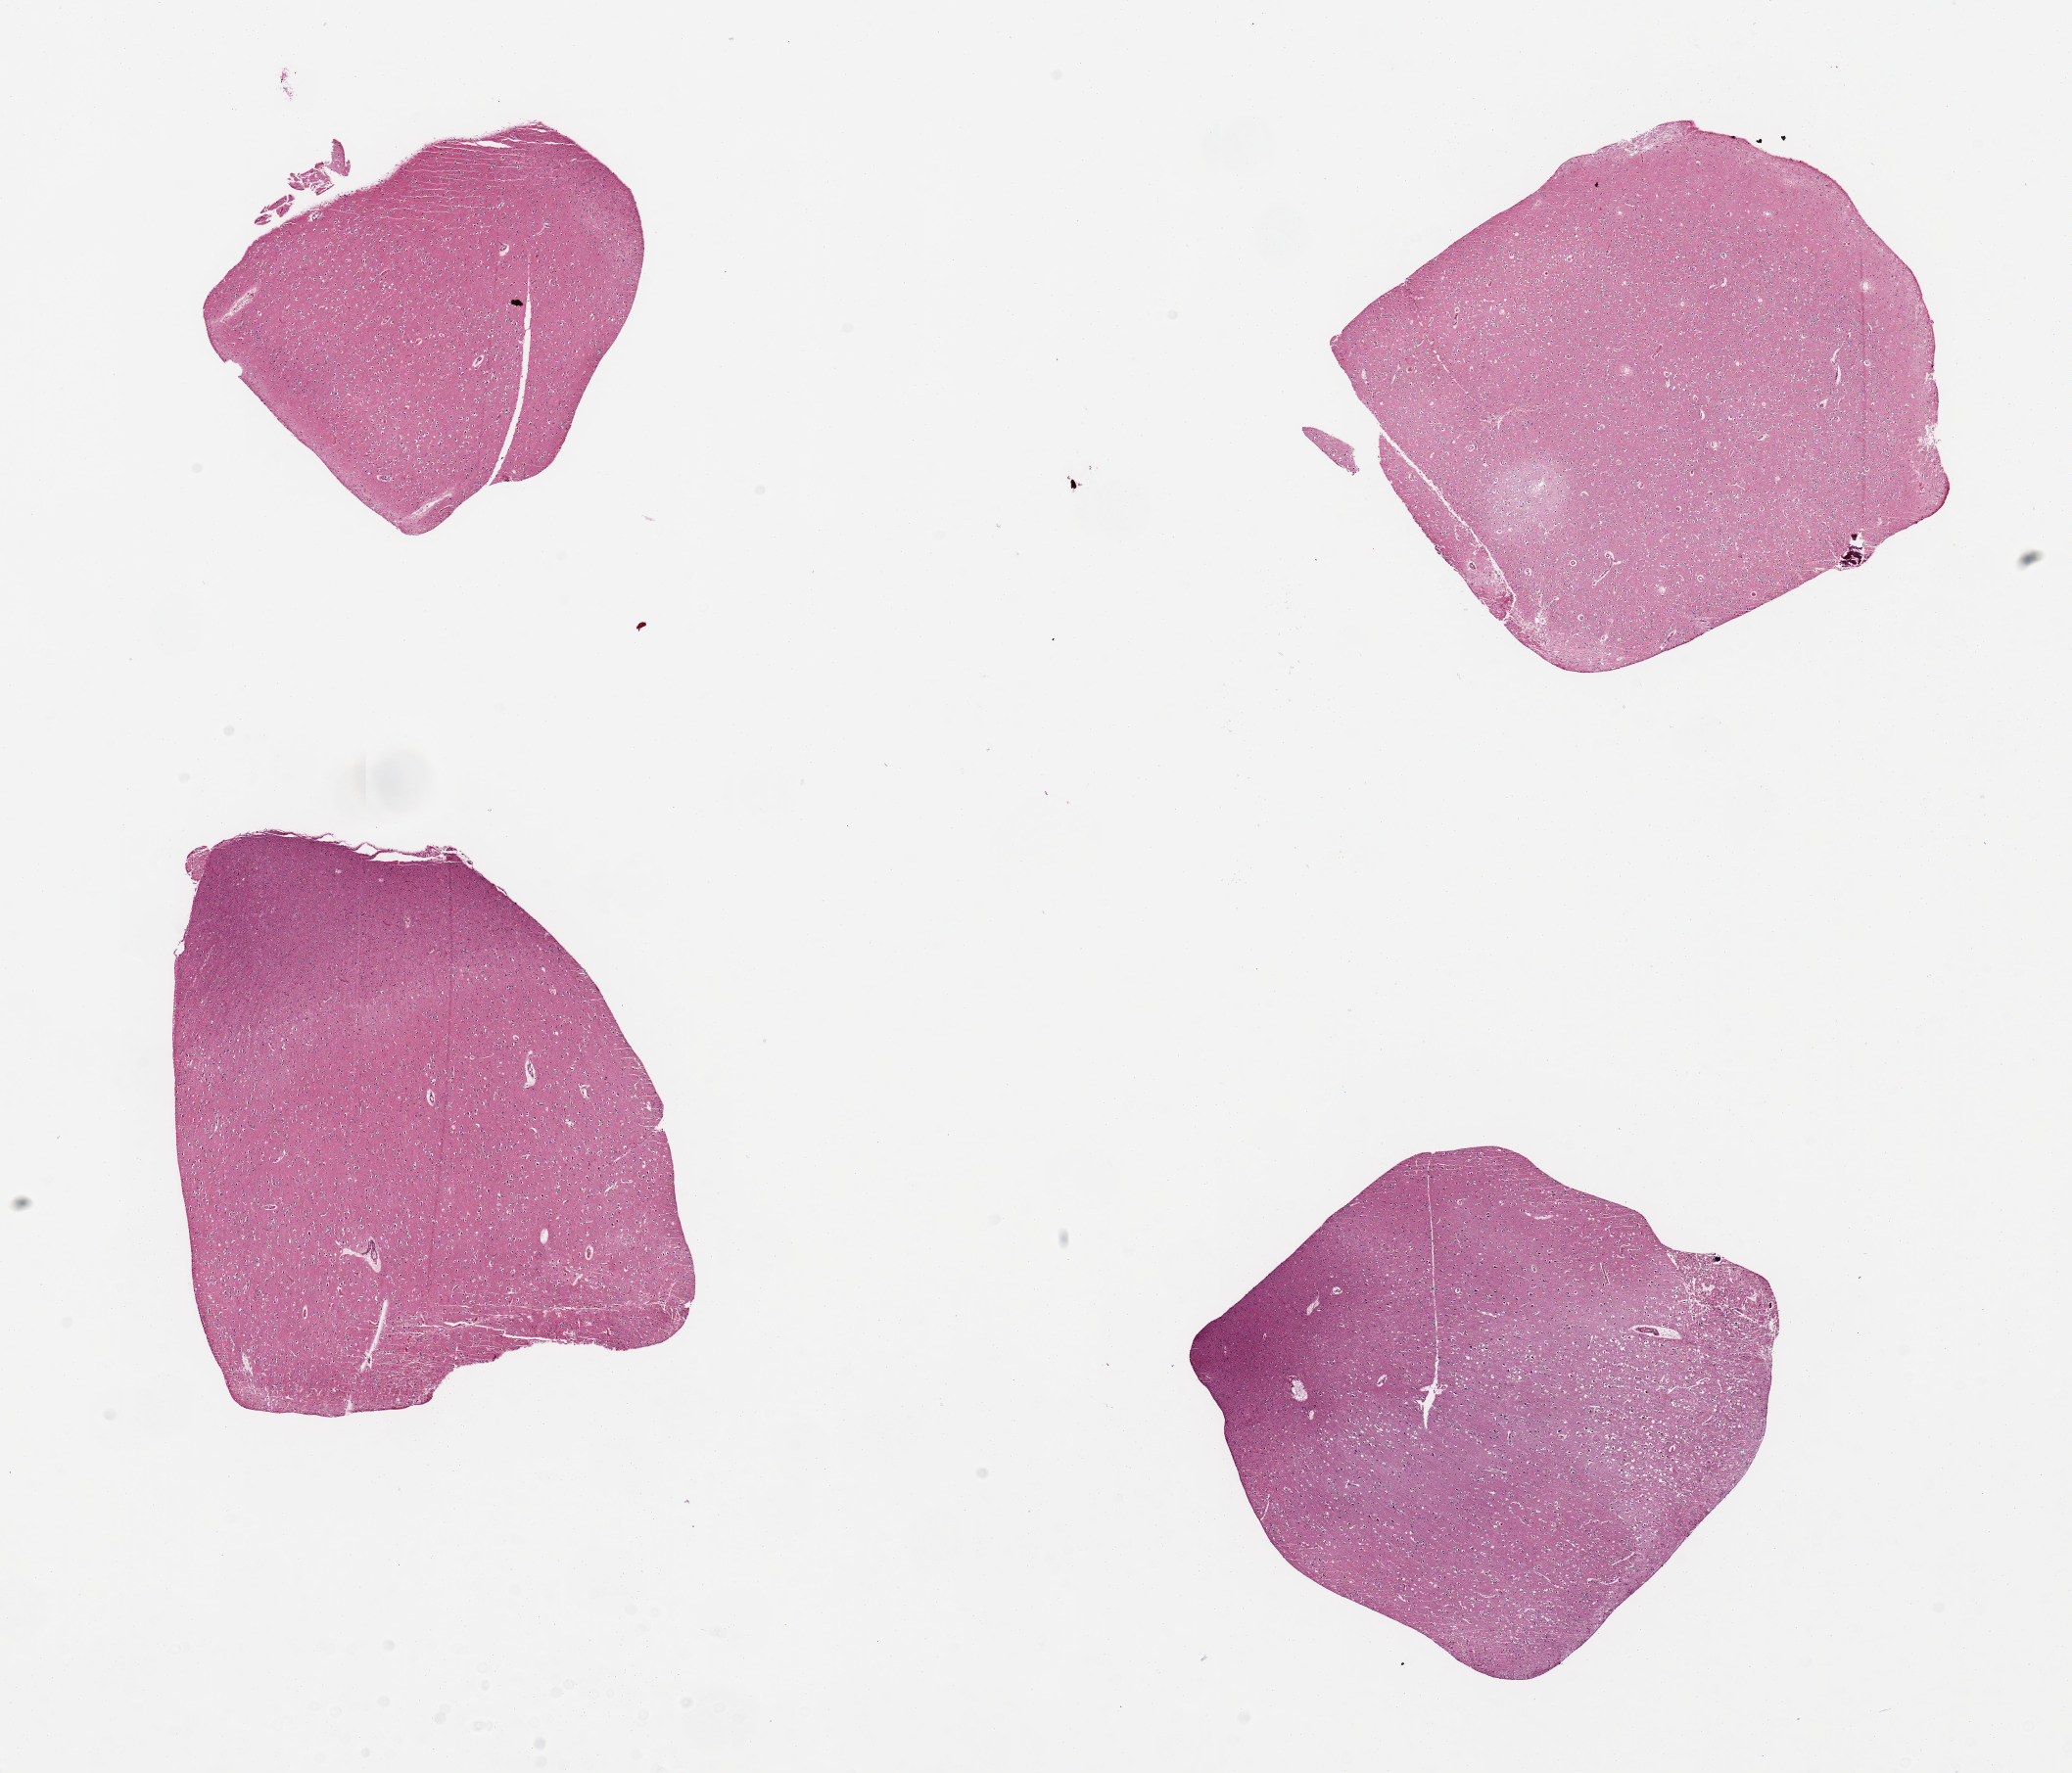
Digitized H&E-stained section — a low-resolution overview of the entire scanned area, about 16.7 x 14.3 mm. PAXgene-fixed, paraffin-embedded tissue. Target tissue: cerebral cortex. Tissue donor sample. Donor sex: female.
Pathologist's review note for this sample: 4 pieces, no abnormalities.